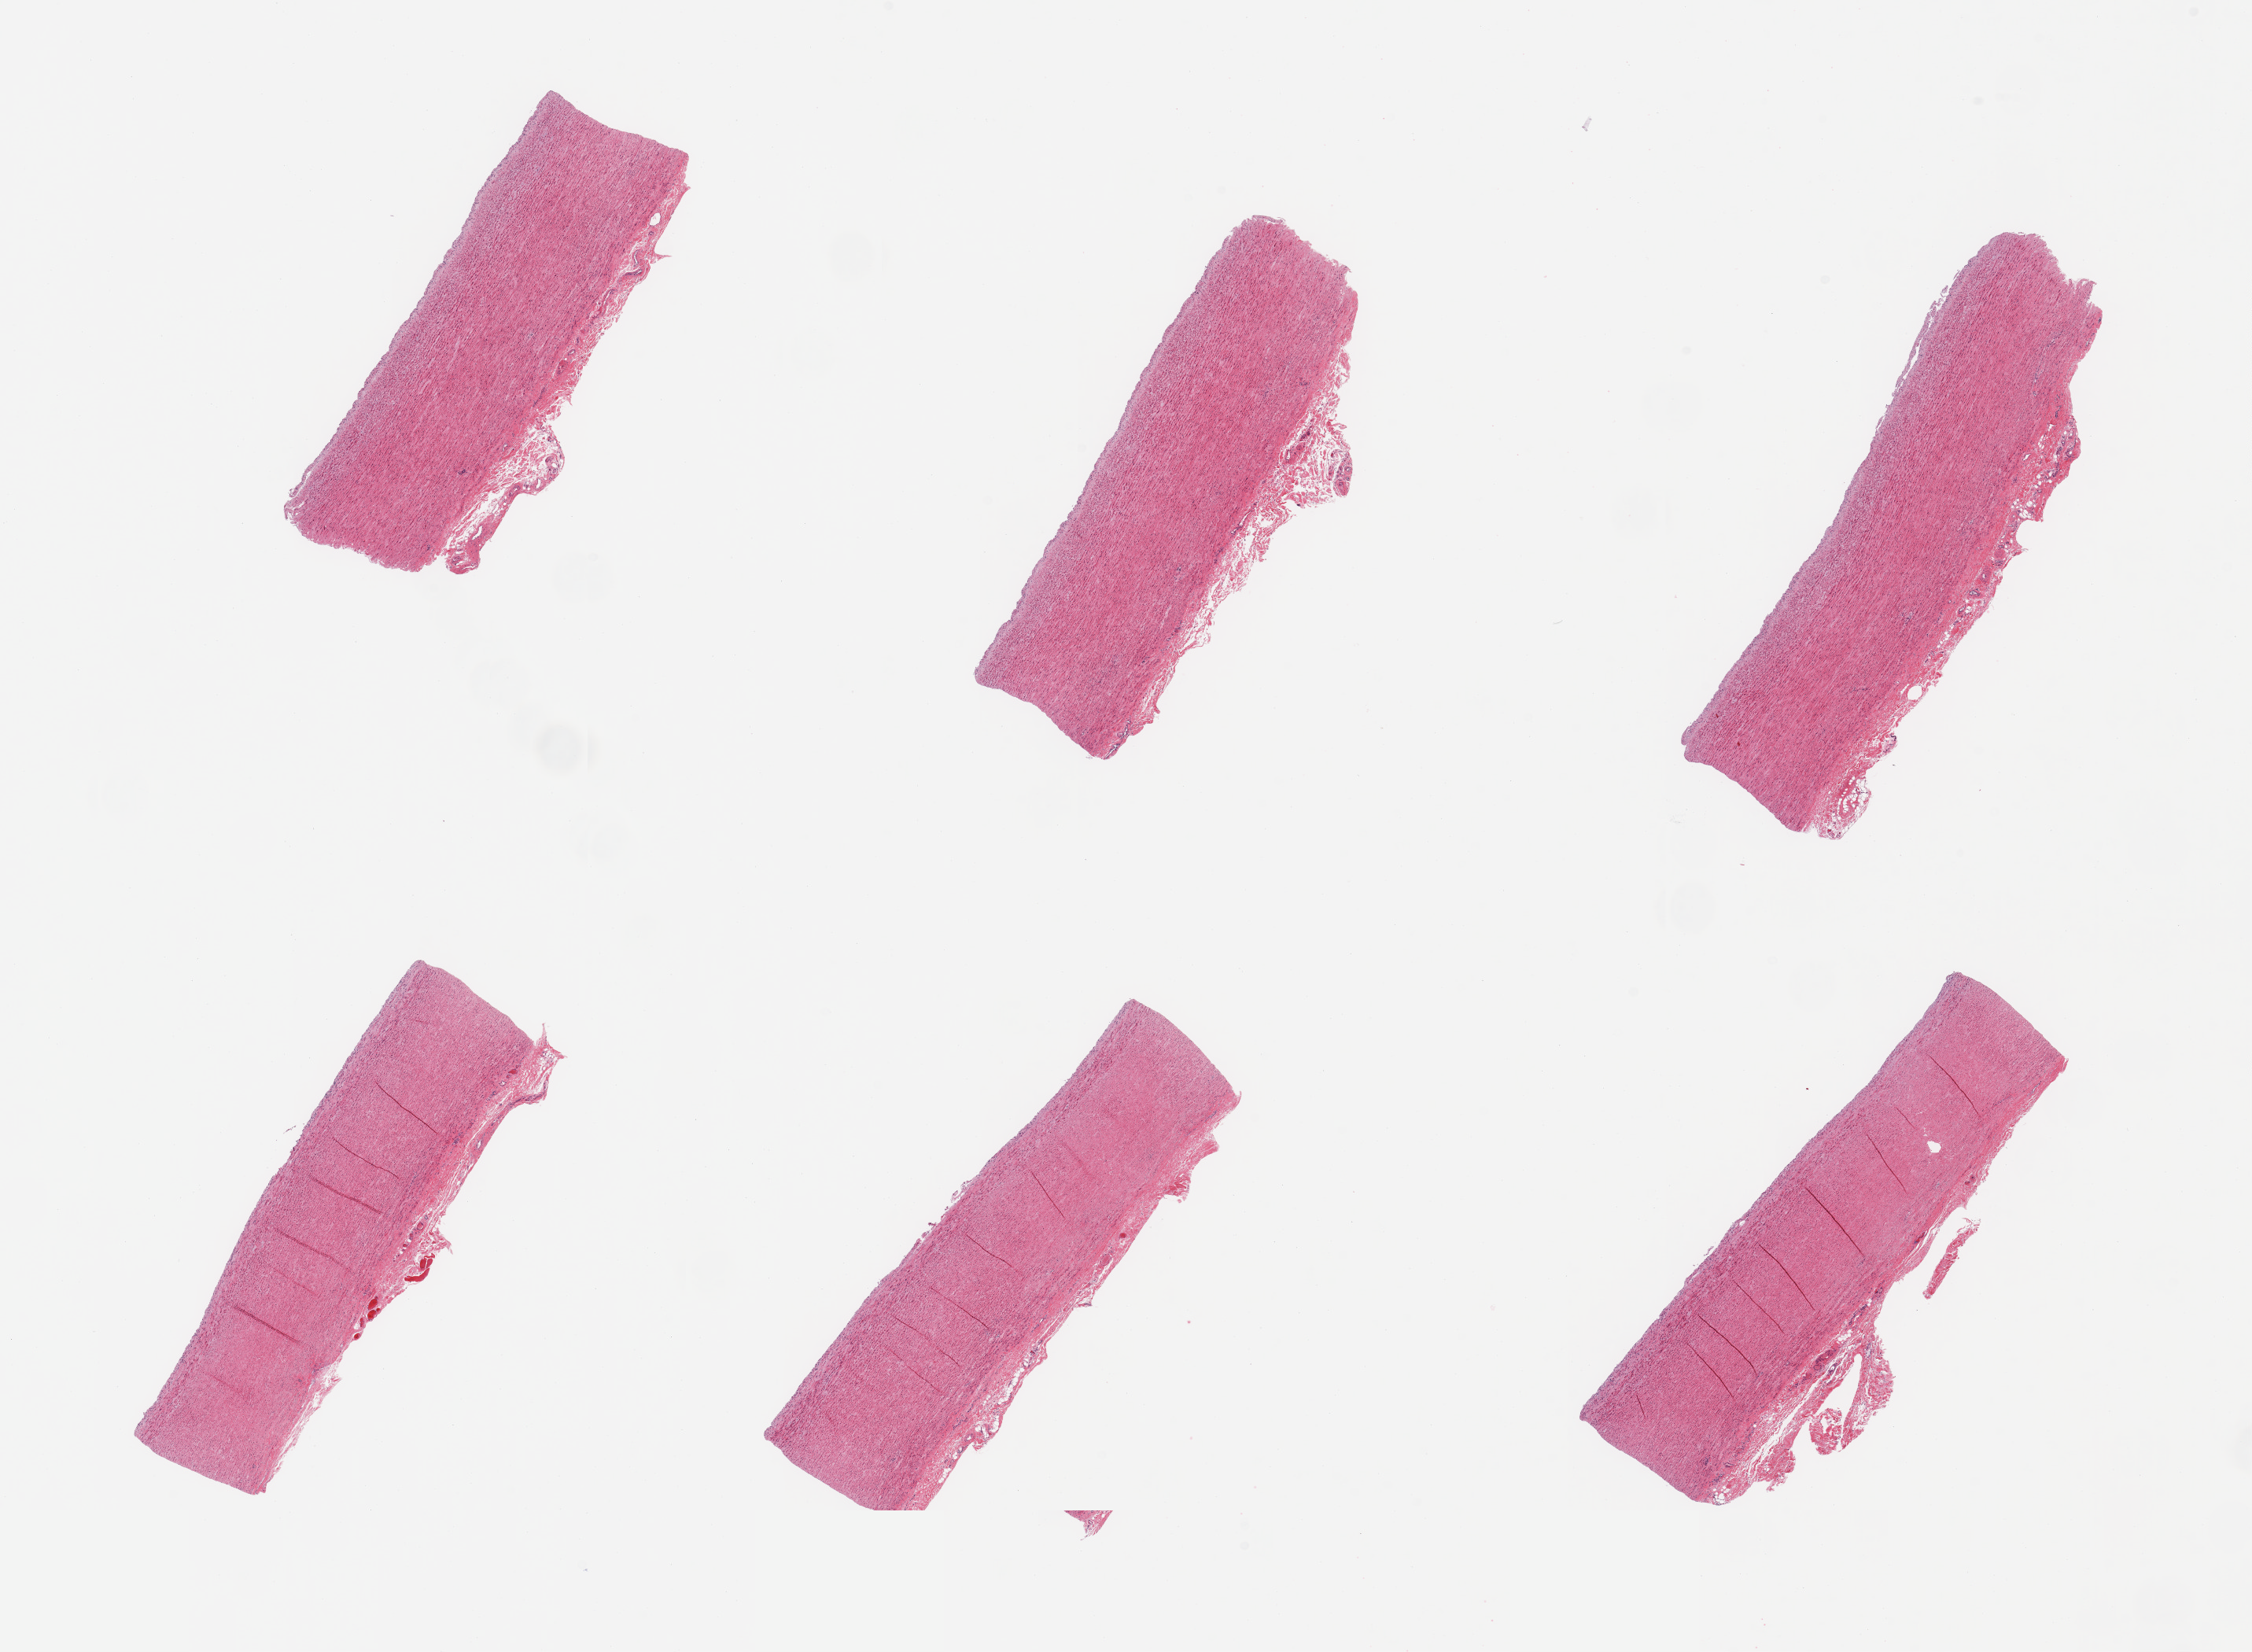
H&E whole-slide image, brightfield — whole scanned area (about 22.6 x 16.6 mm) shown as a low-resolution overview. PAXgene-fixed, paraffin-embedded tissue. Sampled site (target tissue): aorta. Tissue donor sample. Donor: male.
Reviewer comment on this tissue sample: 6 pieces; up to 0.7mm attached adventitia; no atherosclerosis.